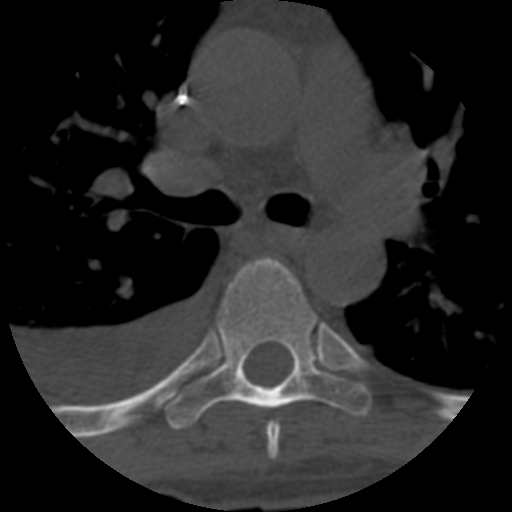
CT including the spine, one axial slice. Position 439 of 708 along the scan axis. Reconstruction kernel STANDARD. One of 3 acquisitions stored at this slice position. Bone window (W 1800 / L 400 HU). 1.25 mm slice thickness. 512 × 512 image matrix. Patient age 55 years. Case-level facts recorded for this patient, not image findings: primary cancer: colon.
Annotated regions visible in this slice (semi-automatically segmented with operator editing):
- T5 vertebra: bounding box [x1, y1, x2, y2] px = [266, 422, 280, 460]
- T6 vertebra: [166, 258, 372, 430]